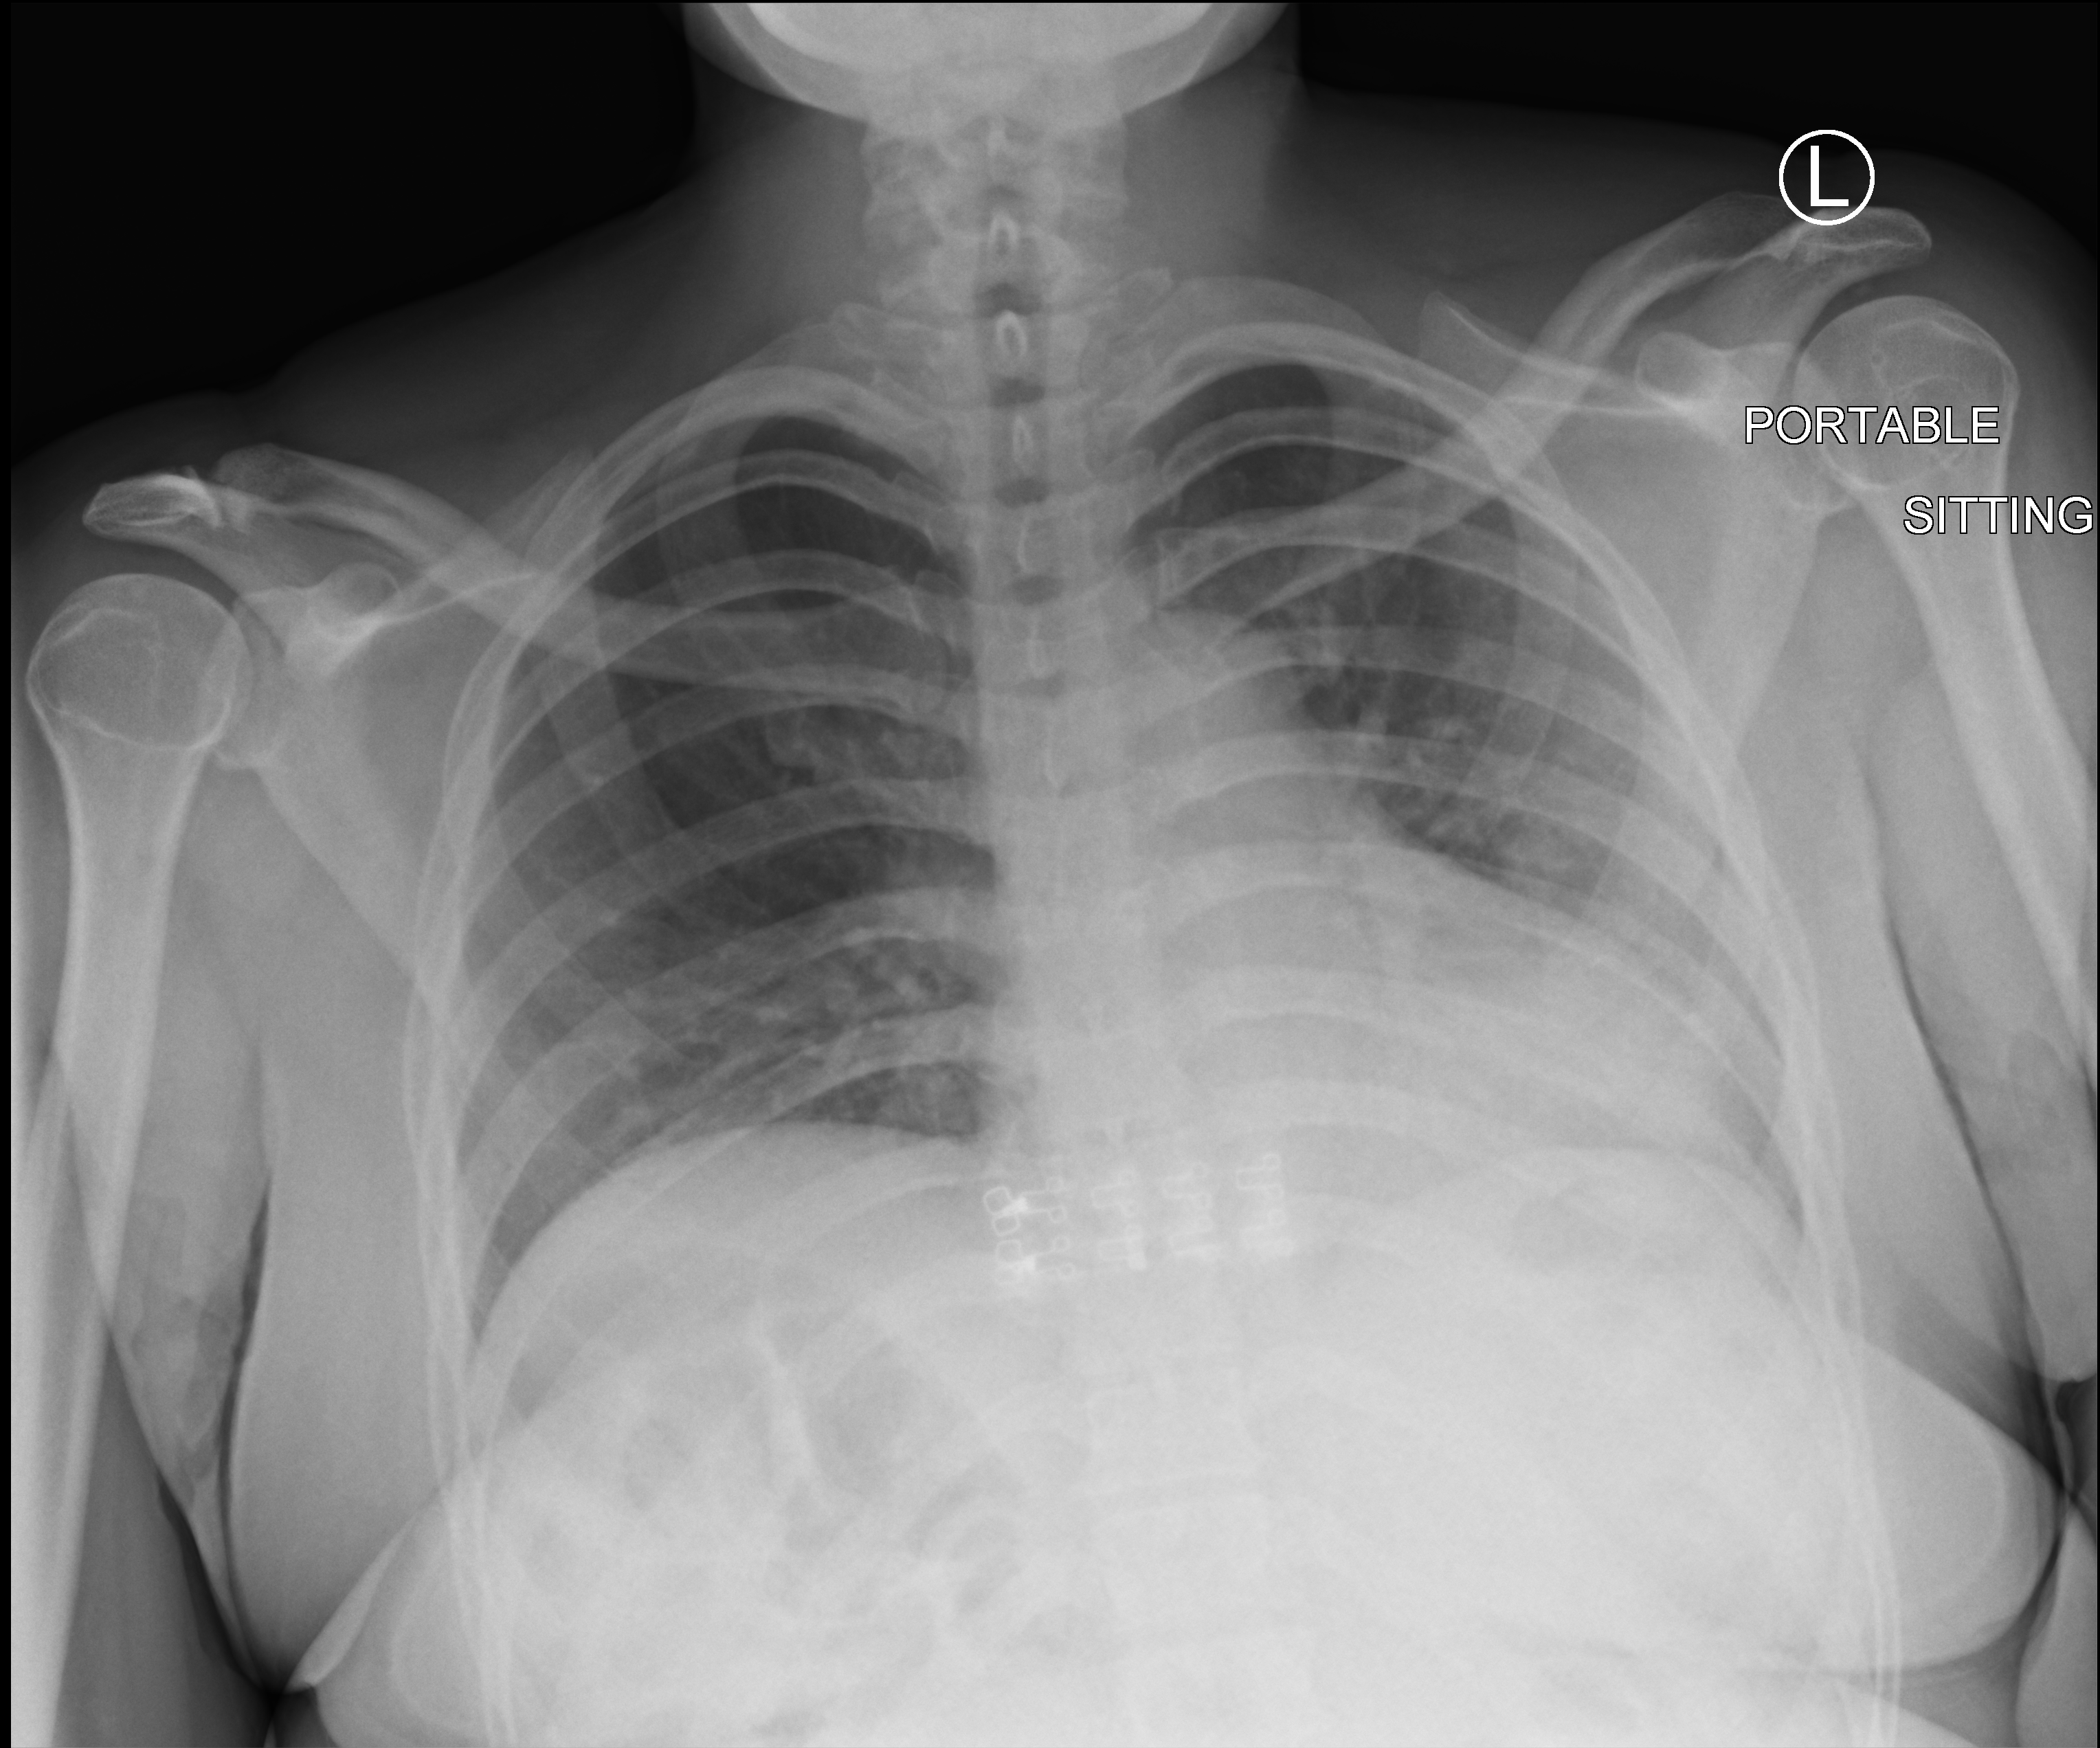
Bedside chest radiograph (computed radiography); anteroposterior (AP) projection. Female patient hospitalised with COVID-19, age 18–59 years.
Hospital-stay facts (about this admission, not read from this image; timing relative to this image not recorded): mechanically ventilated during this hospital stay: no; admitted to intensive care during this hospital stay: no.